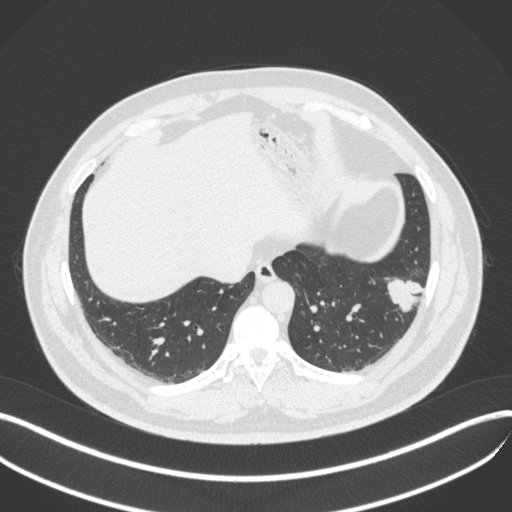
Chest CT, one axial slice; position 117 of 420 along the scan axis; reconstruction kernel B31f; 120 kVp; lung window (W 1500 / L -600 HU); 1 mm slice thickness; 512 × 512 image matrix. Patient: male, 39 years. From the clinical record (not read from this slice): clinical TNM (as recorded): T2a N0 M0.
Outlined on this slice (rectangle marked by the reading radiologist):
- lung tumour (recorded histology: adenocarcinoma): bounding box [x1, y1, x2, y2] px = [383, 271, 427, 319]